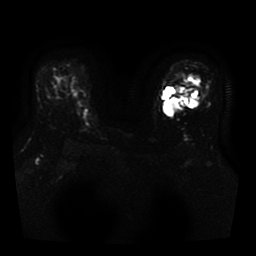
Breast MRI, one axial slice; slice 28 of 41 in the series (ordered by position); diffusion-weighted series; image 2 of 3 stored at this slice position (different b-values; order by instance number); 1.5 T; 5 mm slice thickness; 256 × 256 image matrix. Female patient.
Annotated regions visible in this slice (expert manual segmentation):
- tumour on diffusion-weighted imaging: bounding box <164,92,178,117> (left, top, right, bottom; pixels)